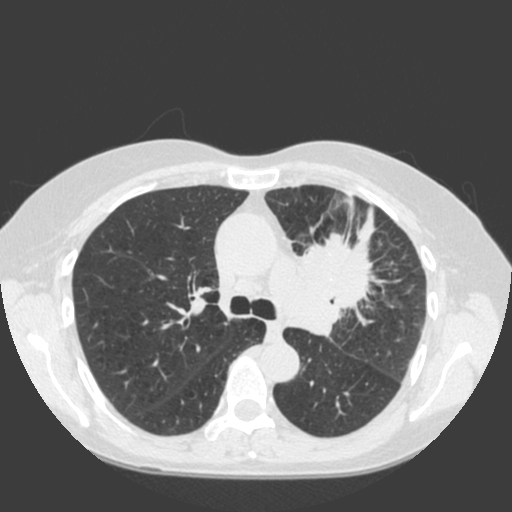
Low-dose screening chest CT, one axial slice. Position 125 of 184 along the scan axis. 120 kVp. Lung window (W 1500 / L -600 HU). 2 mm slice thickness. 512 × 512 image matrix, field of view 350 × 350 mm.
Outlined on this slice (expert manual segmentation):
- lesion 1 (tumor, hilum of left lung): bounding box [x1, y1, x2, y2] px = [287, 208, 384, 334]